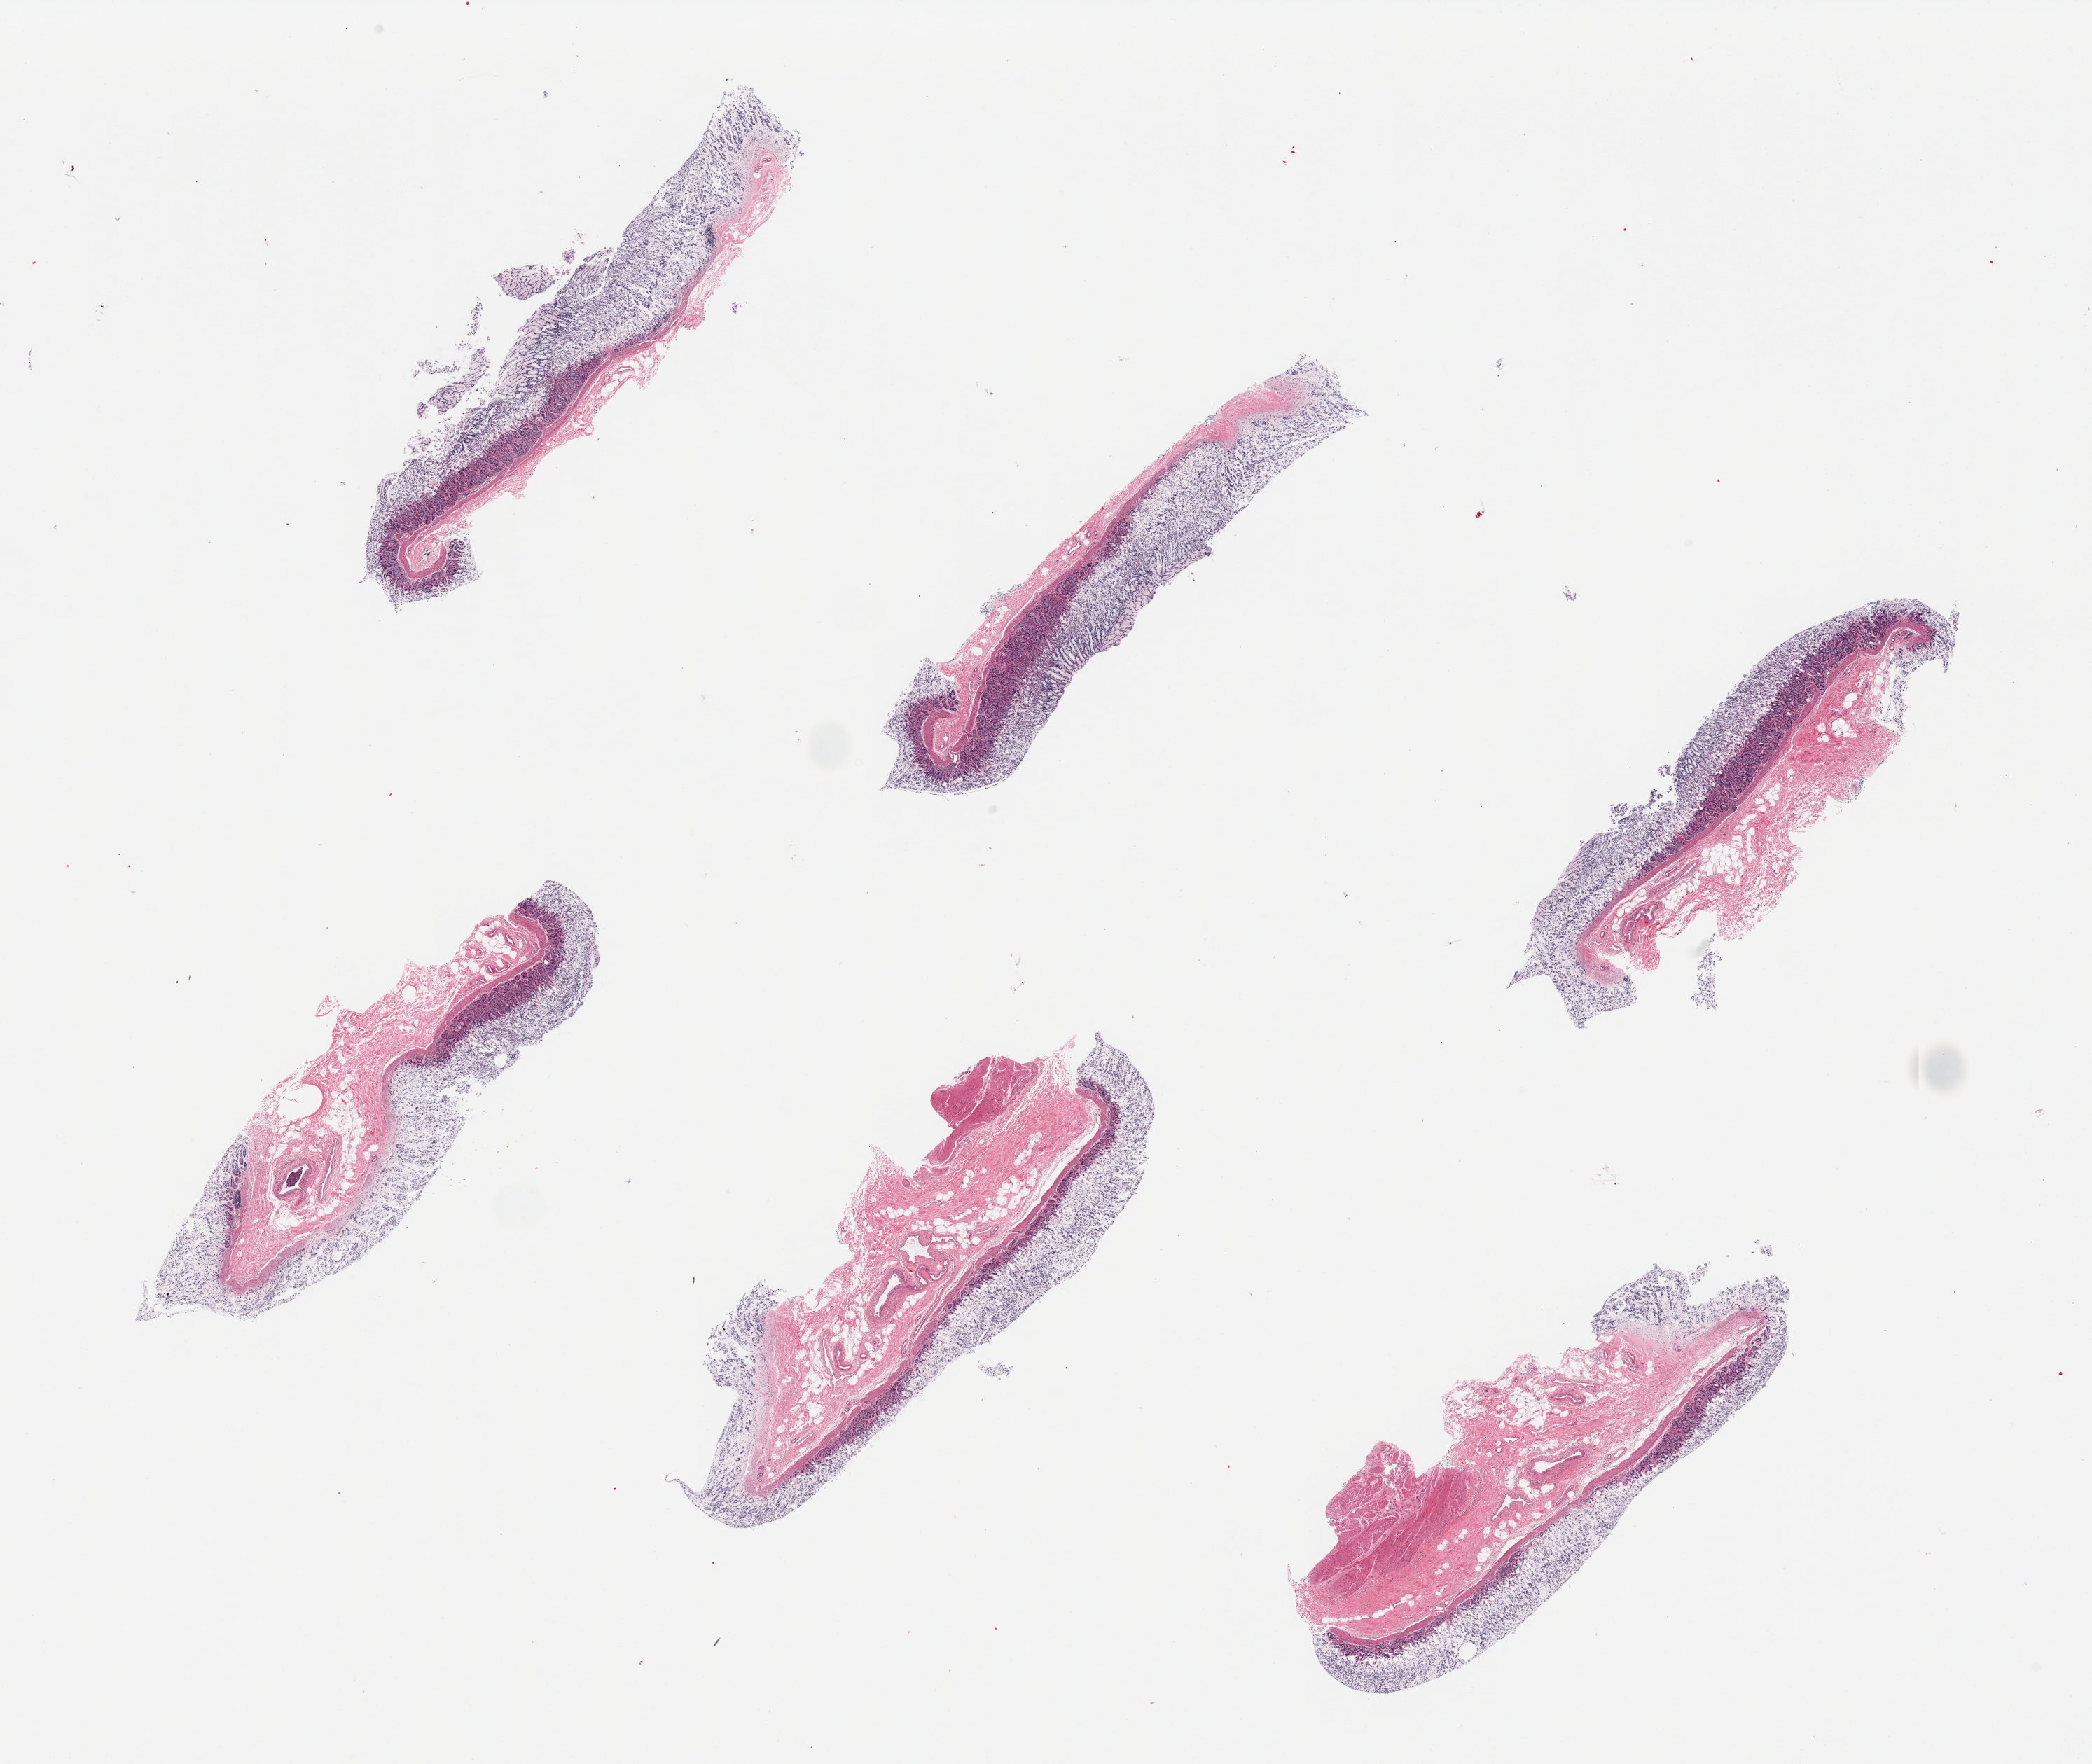
Digitized haematoxylin and eosin-stained section — shown as a low-resolution overview of the whole scanned area (about 23.6 x 19.9 mm, from a 20x scan). PAXgene-fixed paraffin-embedded (PFPE) section. Sampled site (target tissue): stomach. Tissue donor sample. Donor: male.
Review note (as recorded): 6 pieces. Severe surface autolysis; some preservation of deep glands.